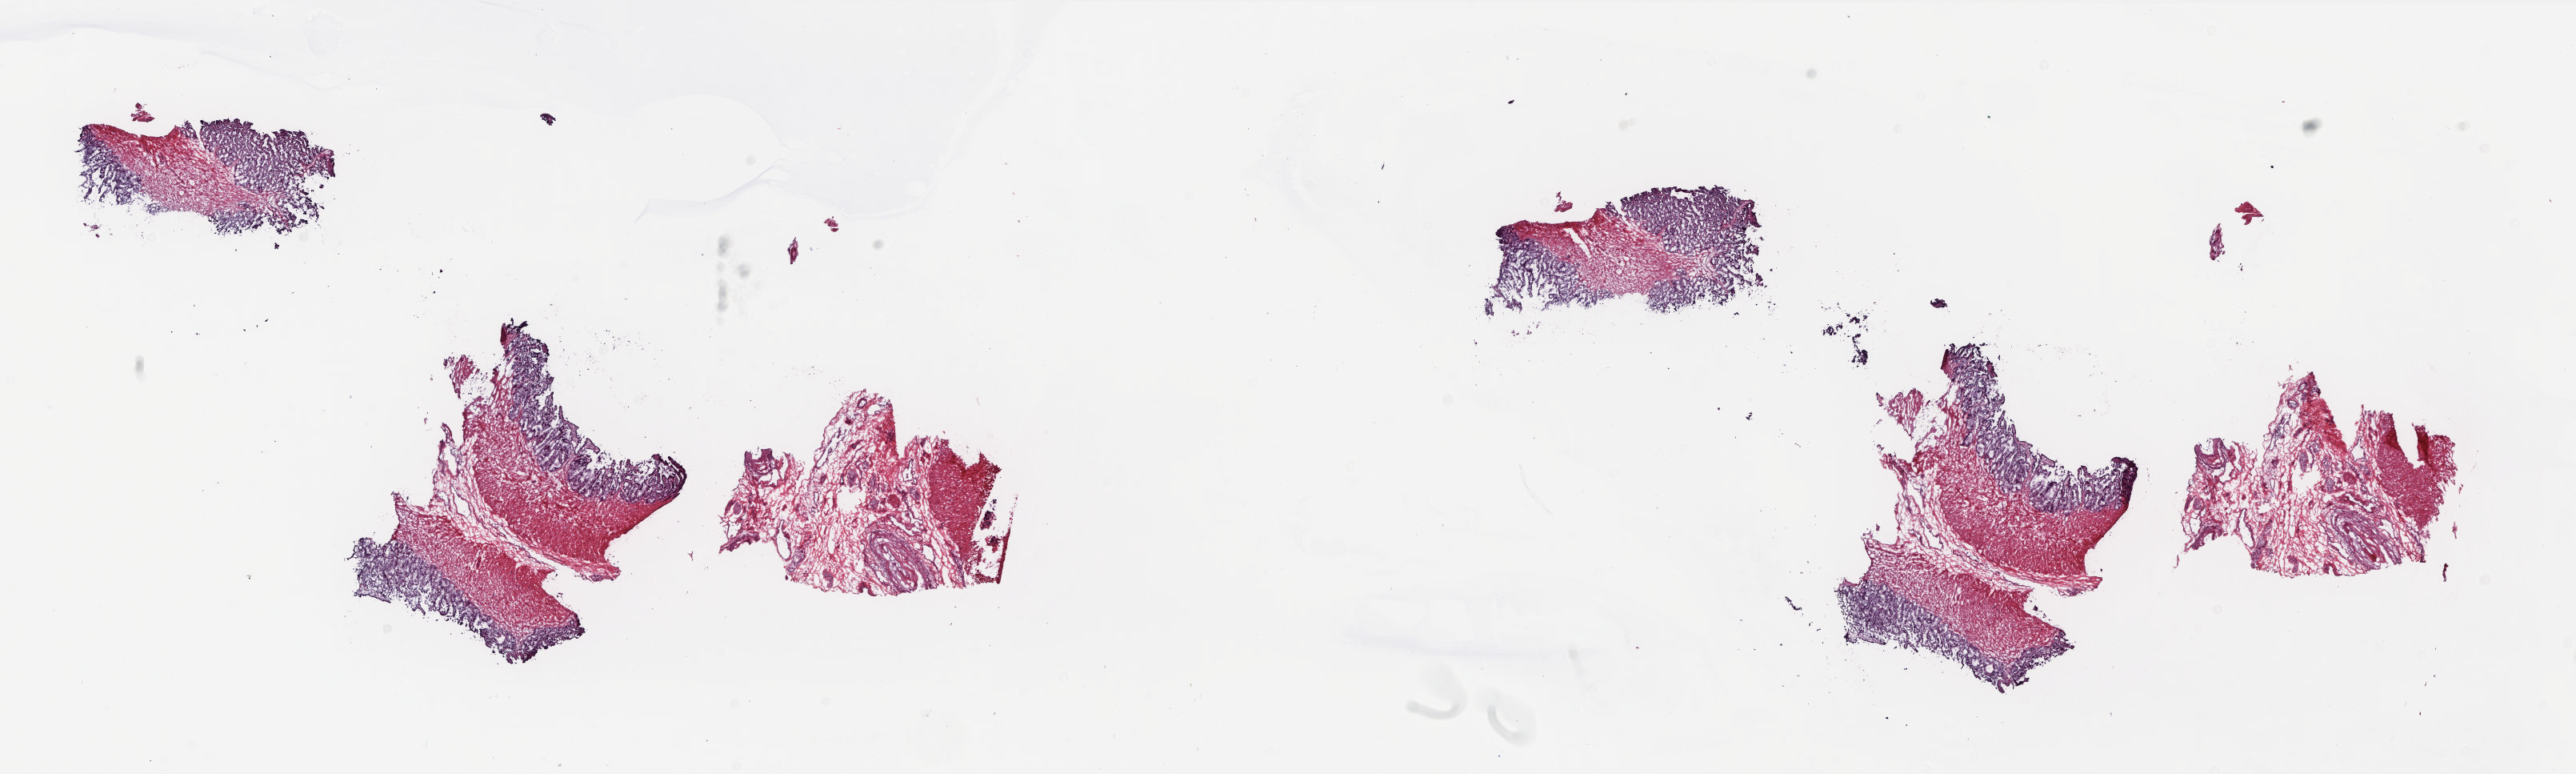
H&E whole-slide image, low-resolution overview of the scanned area, about 26.0 x 7.8 mm (from a 20x scan). Frozen section from the top of the tissue portion. Solid tissue normal (non-tumour tissue) sample from the prostate. Male patient; age at initial diagnosis 46 years. Composition of this section per pathologist review: tumour cells 0%, tumour nuclei 0%, normal cells 100%, stromal cells 0%, necrosis 0%. Infiltration values recorded for this section: lymphocyte infiltration 1%, monocyte infiltration 0%, neutrophil infiltration 0%.
This section: solid tissue normal sample (biorepository sample class). Patient diagnosis: Adenocarcinoma, NOS (prostate gland).